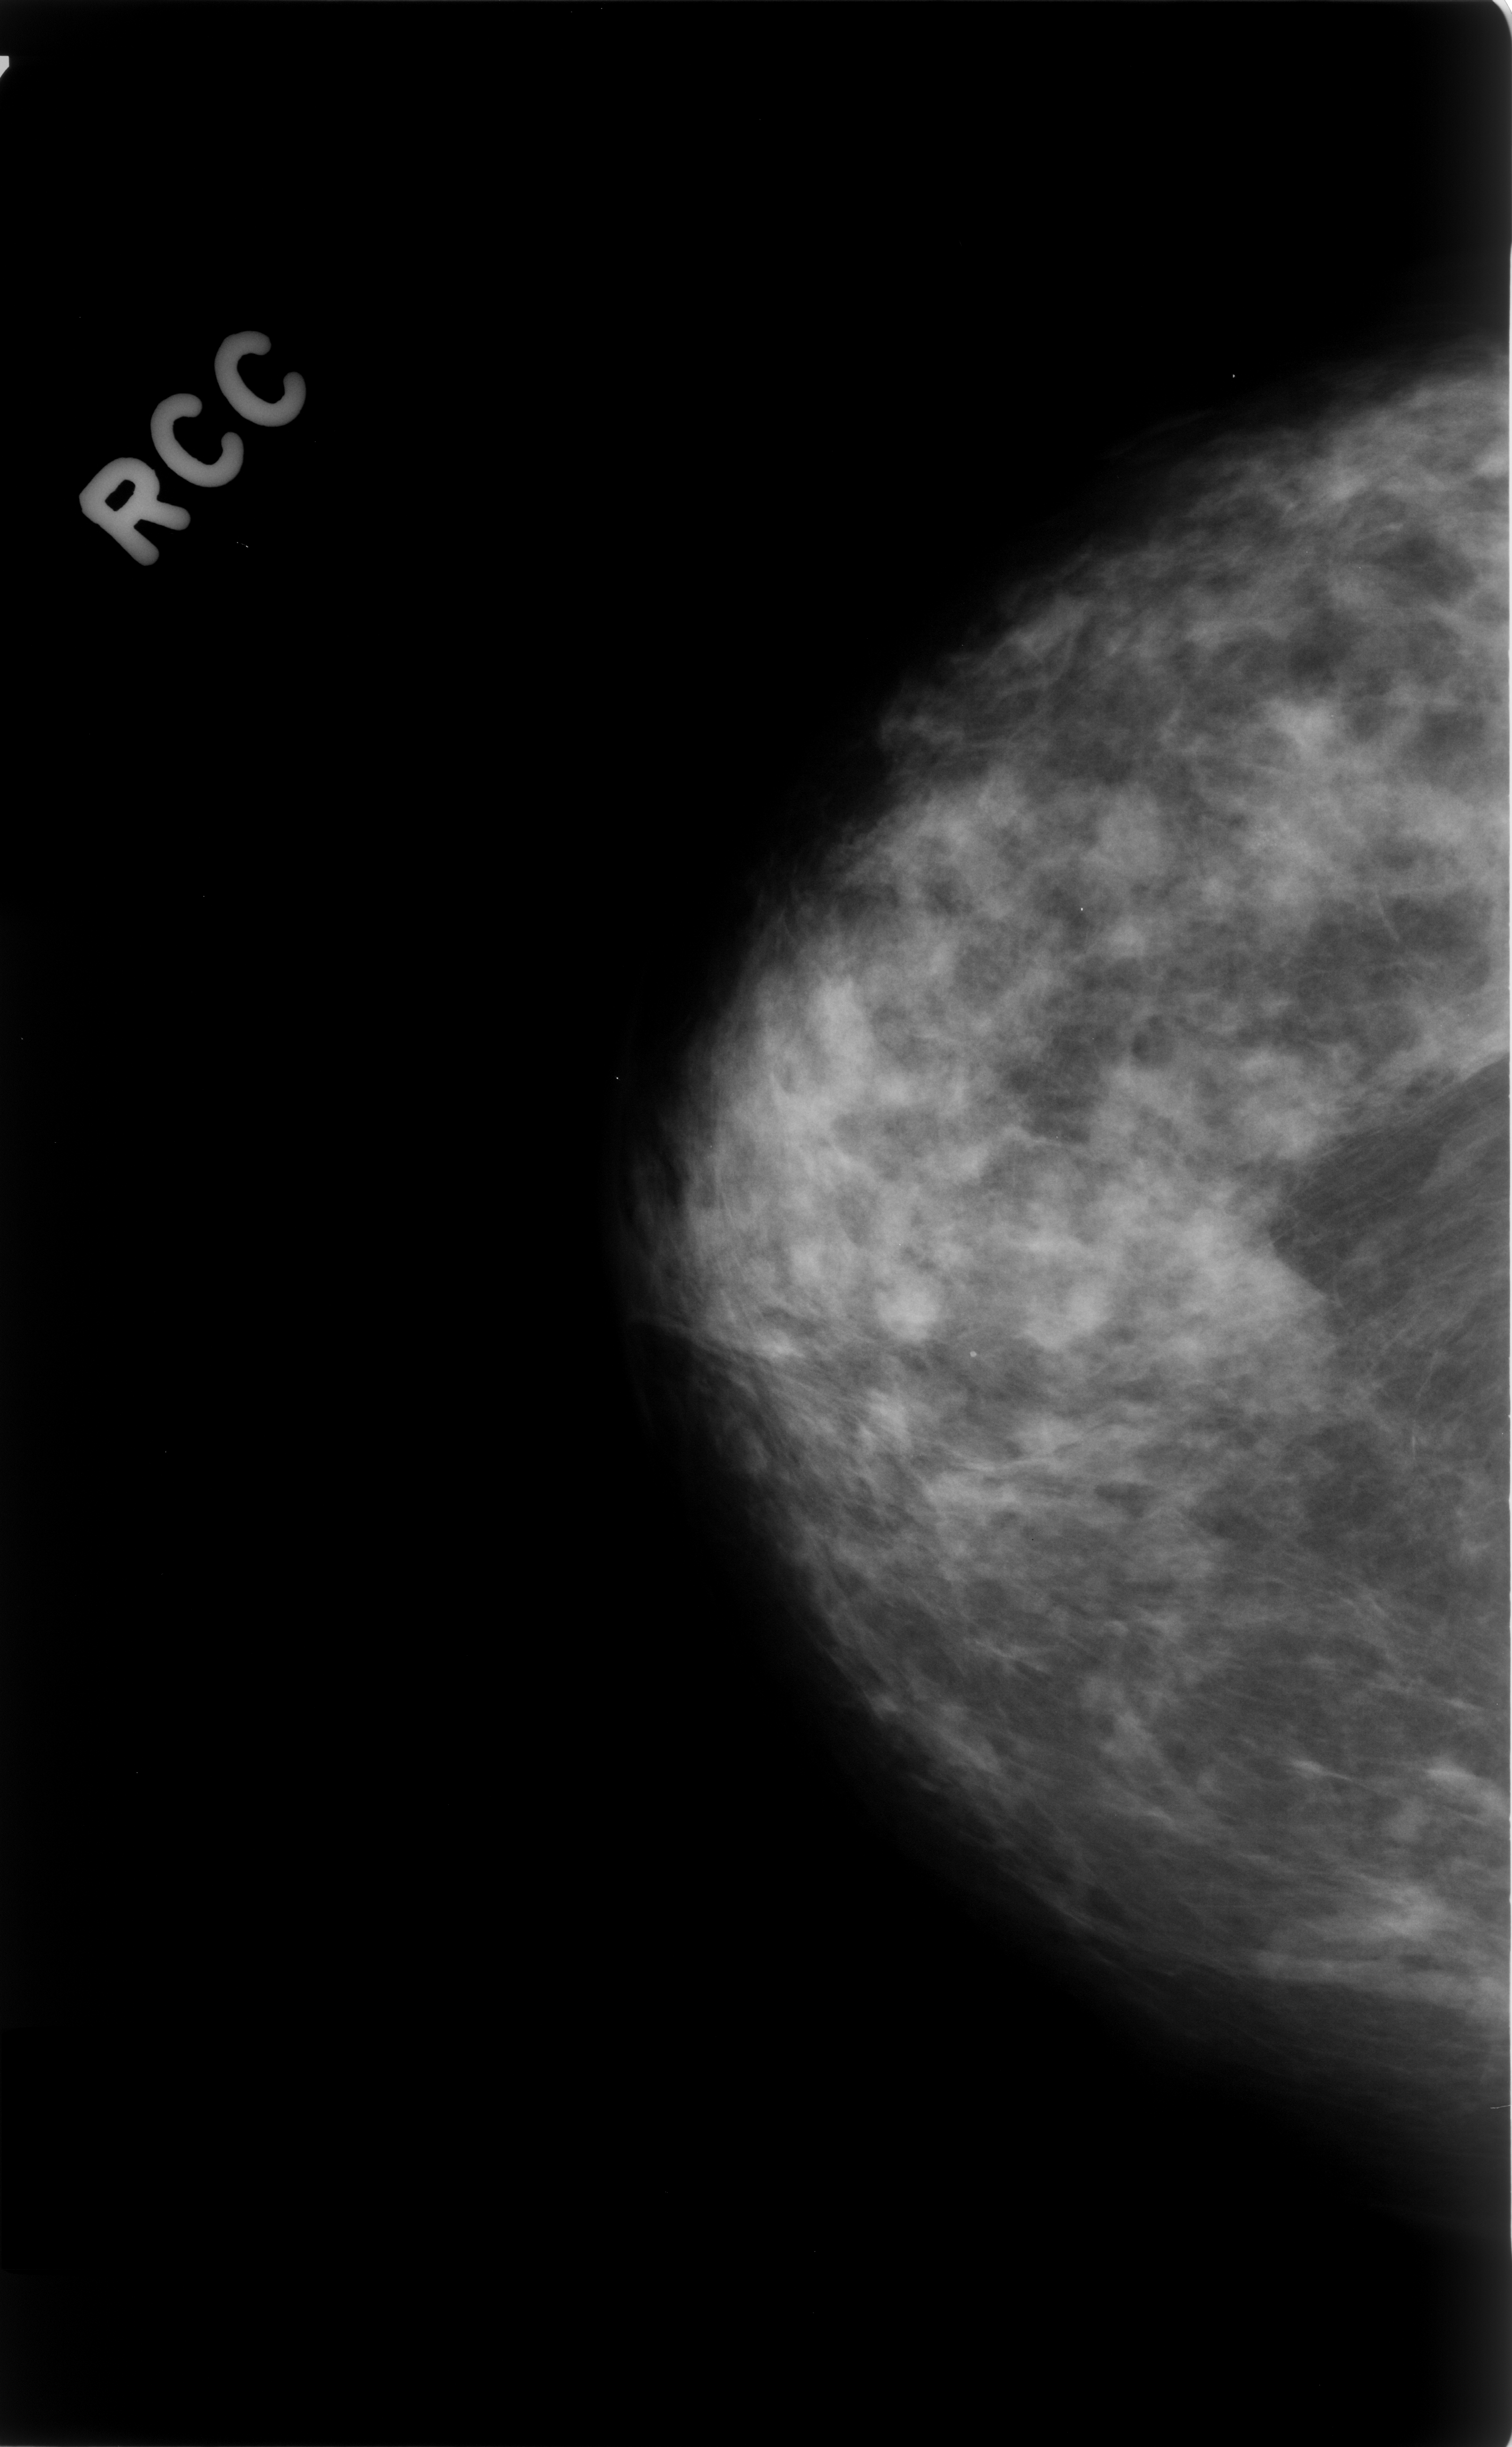
Scanned film-screen mammogram; right breast; CC view; breast composition: scattered fibroglandular densities (BI-RADS density category 2 of 4).
Radiologist-marked abnormalities on this image: calcifications, morphology amorphous, distribution clustered; BI-RADS assessment category 4; subtlety rating 2 on a 1 (subtle) to 5 (obvious) scale; pathology (as recorded): benign.